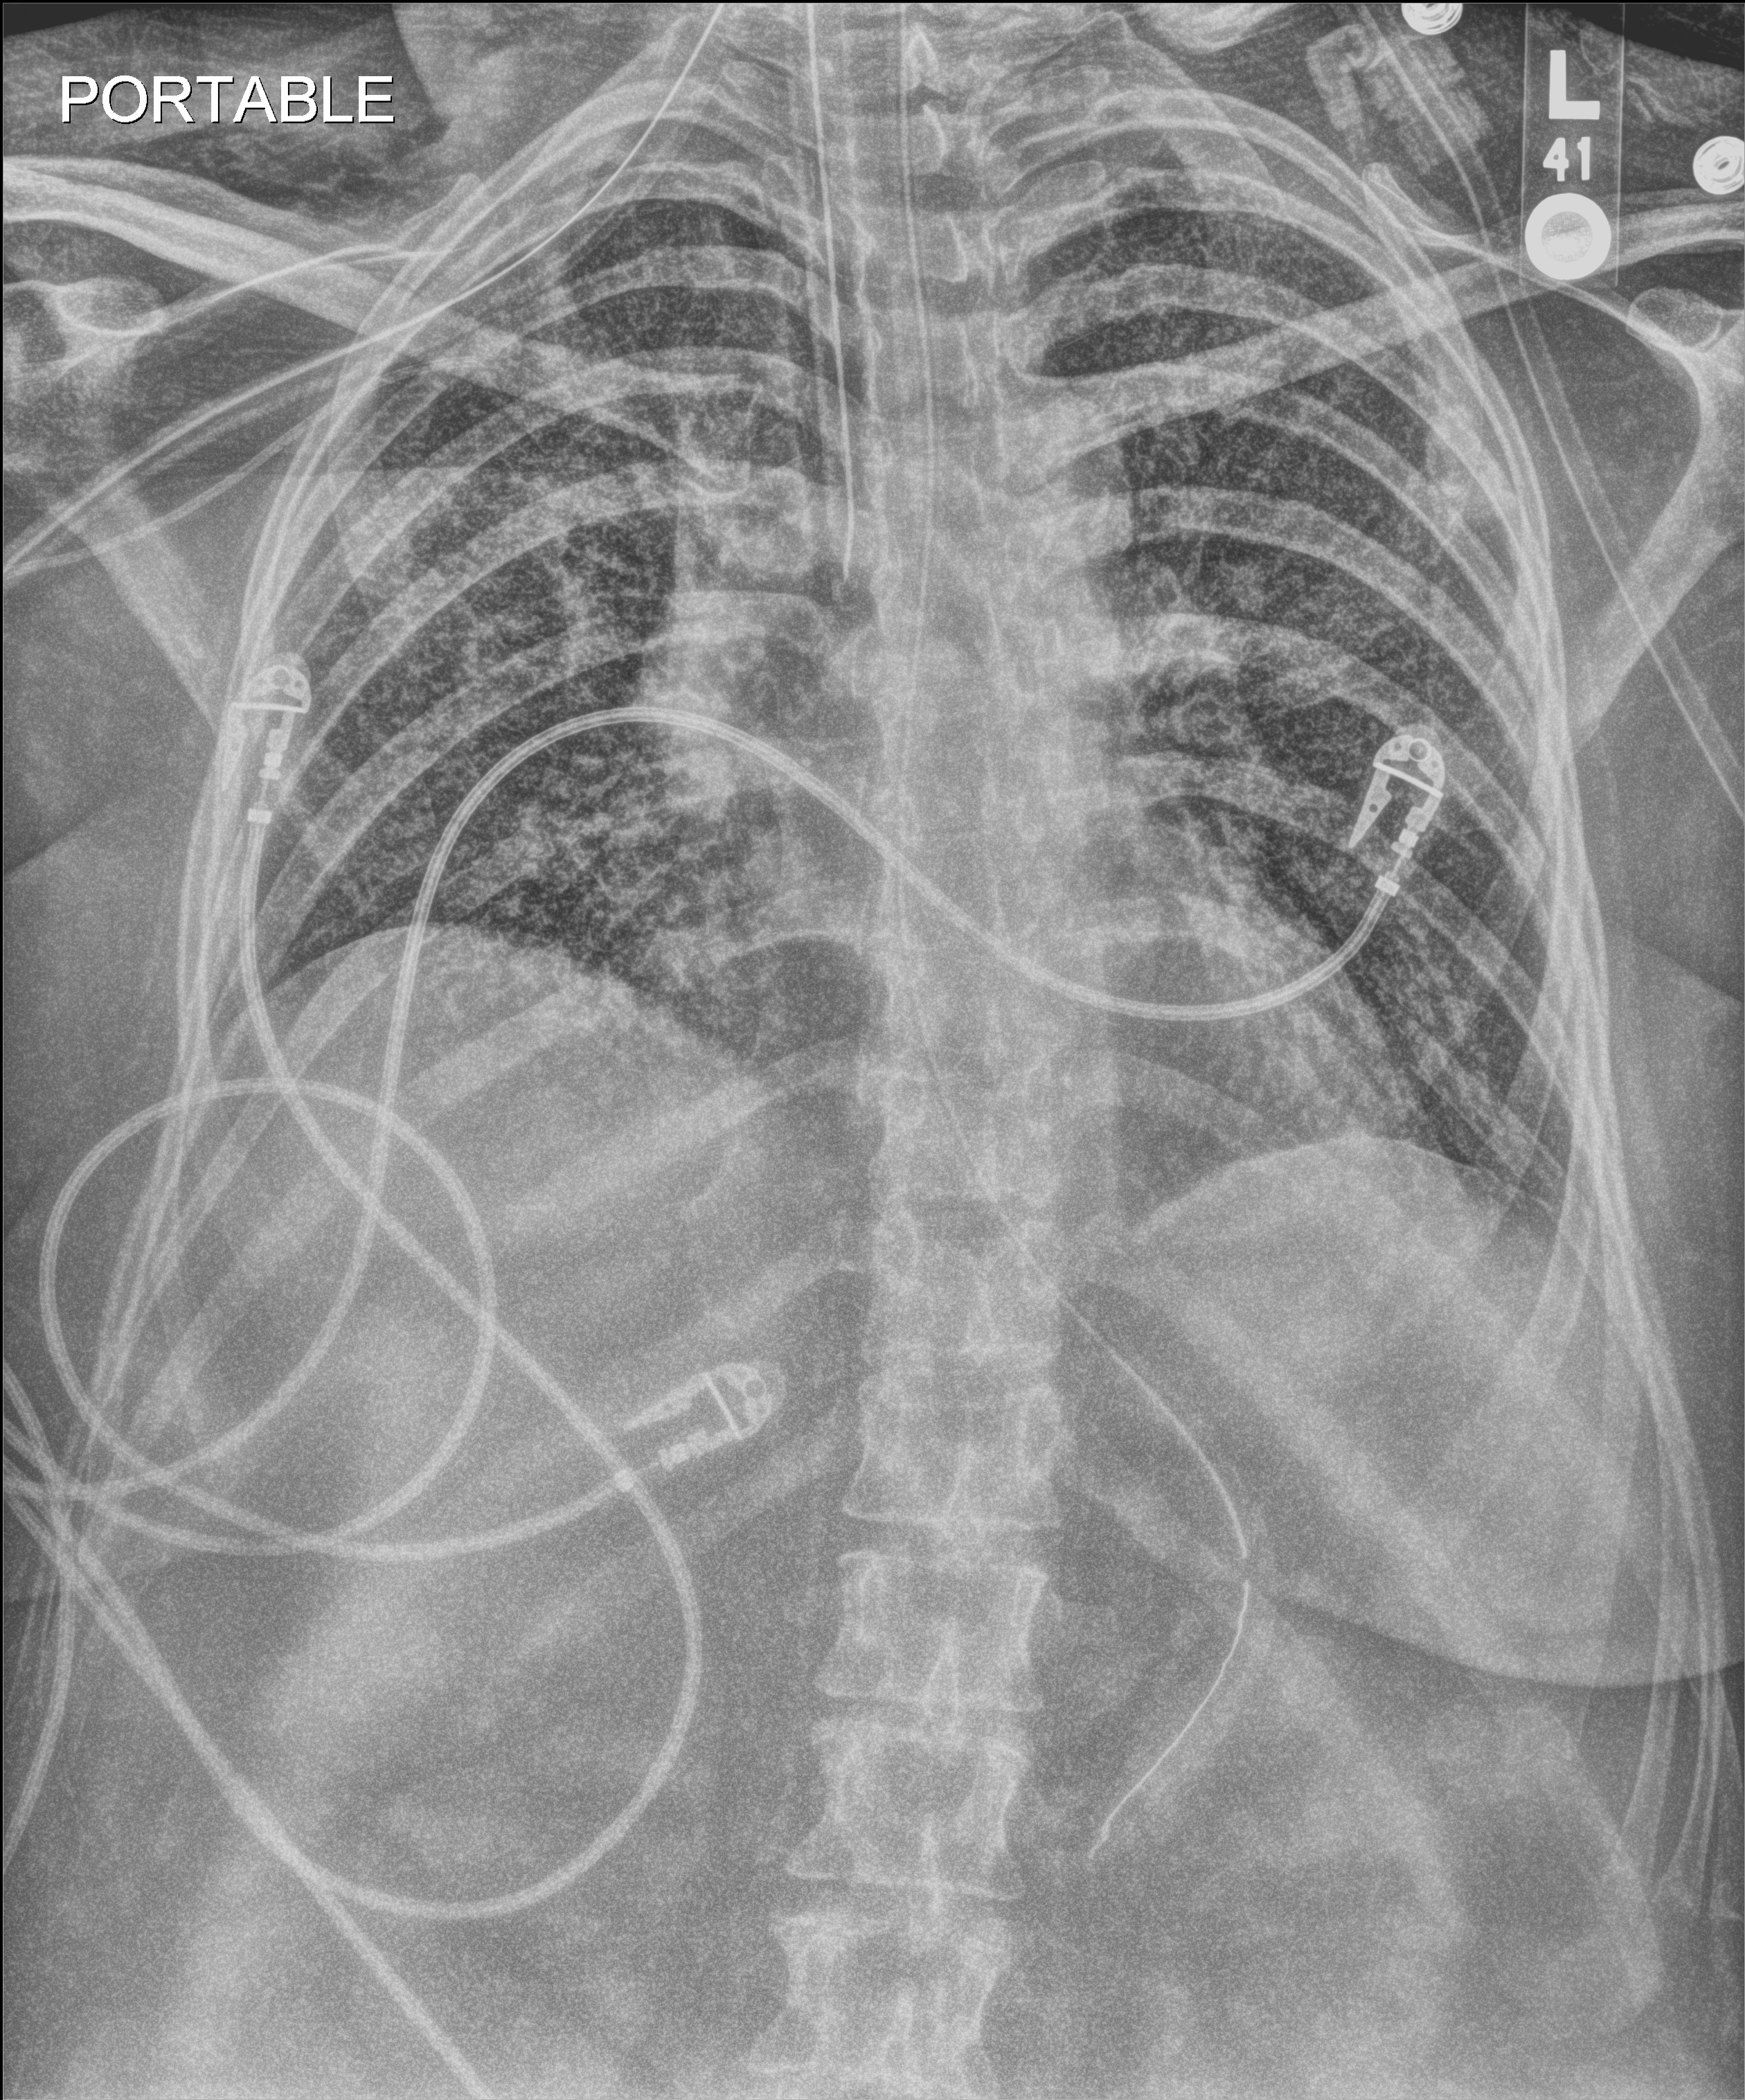
Chest radiograph. Female patient hospitalised with COVID-19, age 18–59 years.
From the hospital-stay record, not from the radiograph (when in the stay this image was taken is not recorded):
- mechanically ventilated during this hospital stay: yes